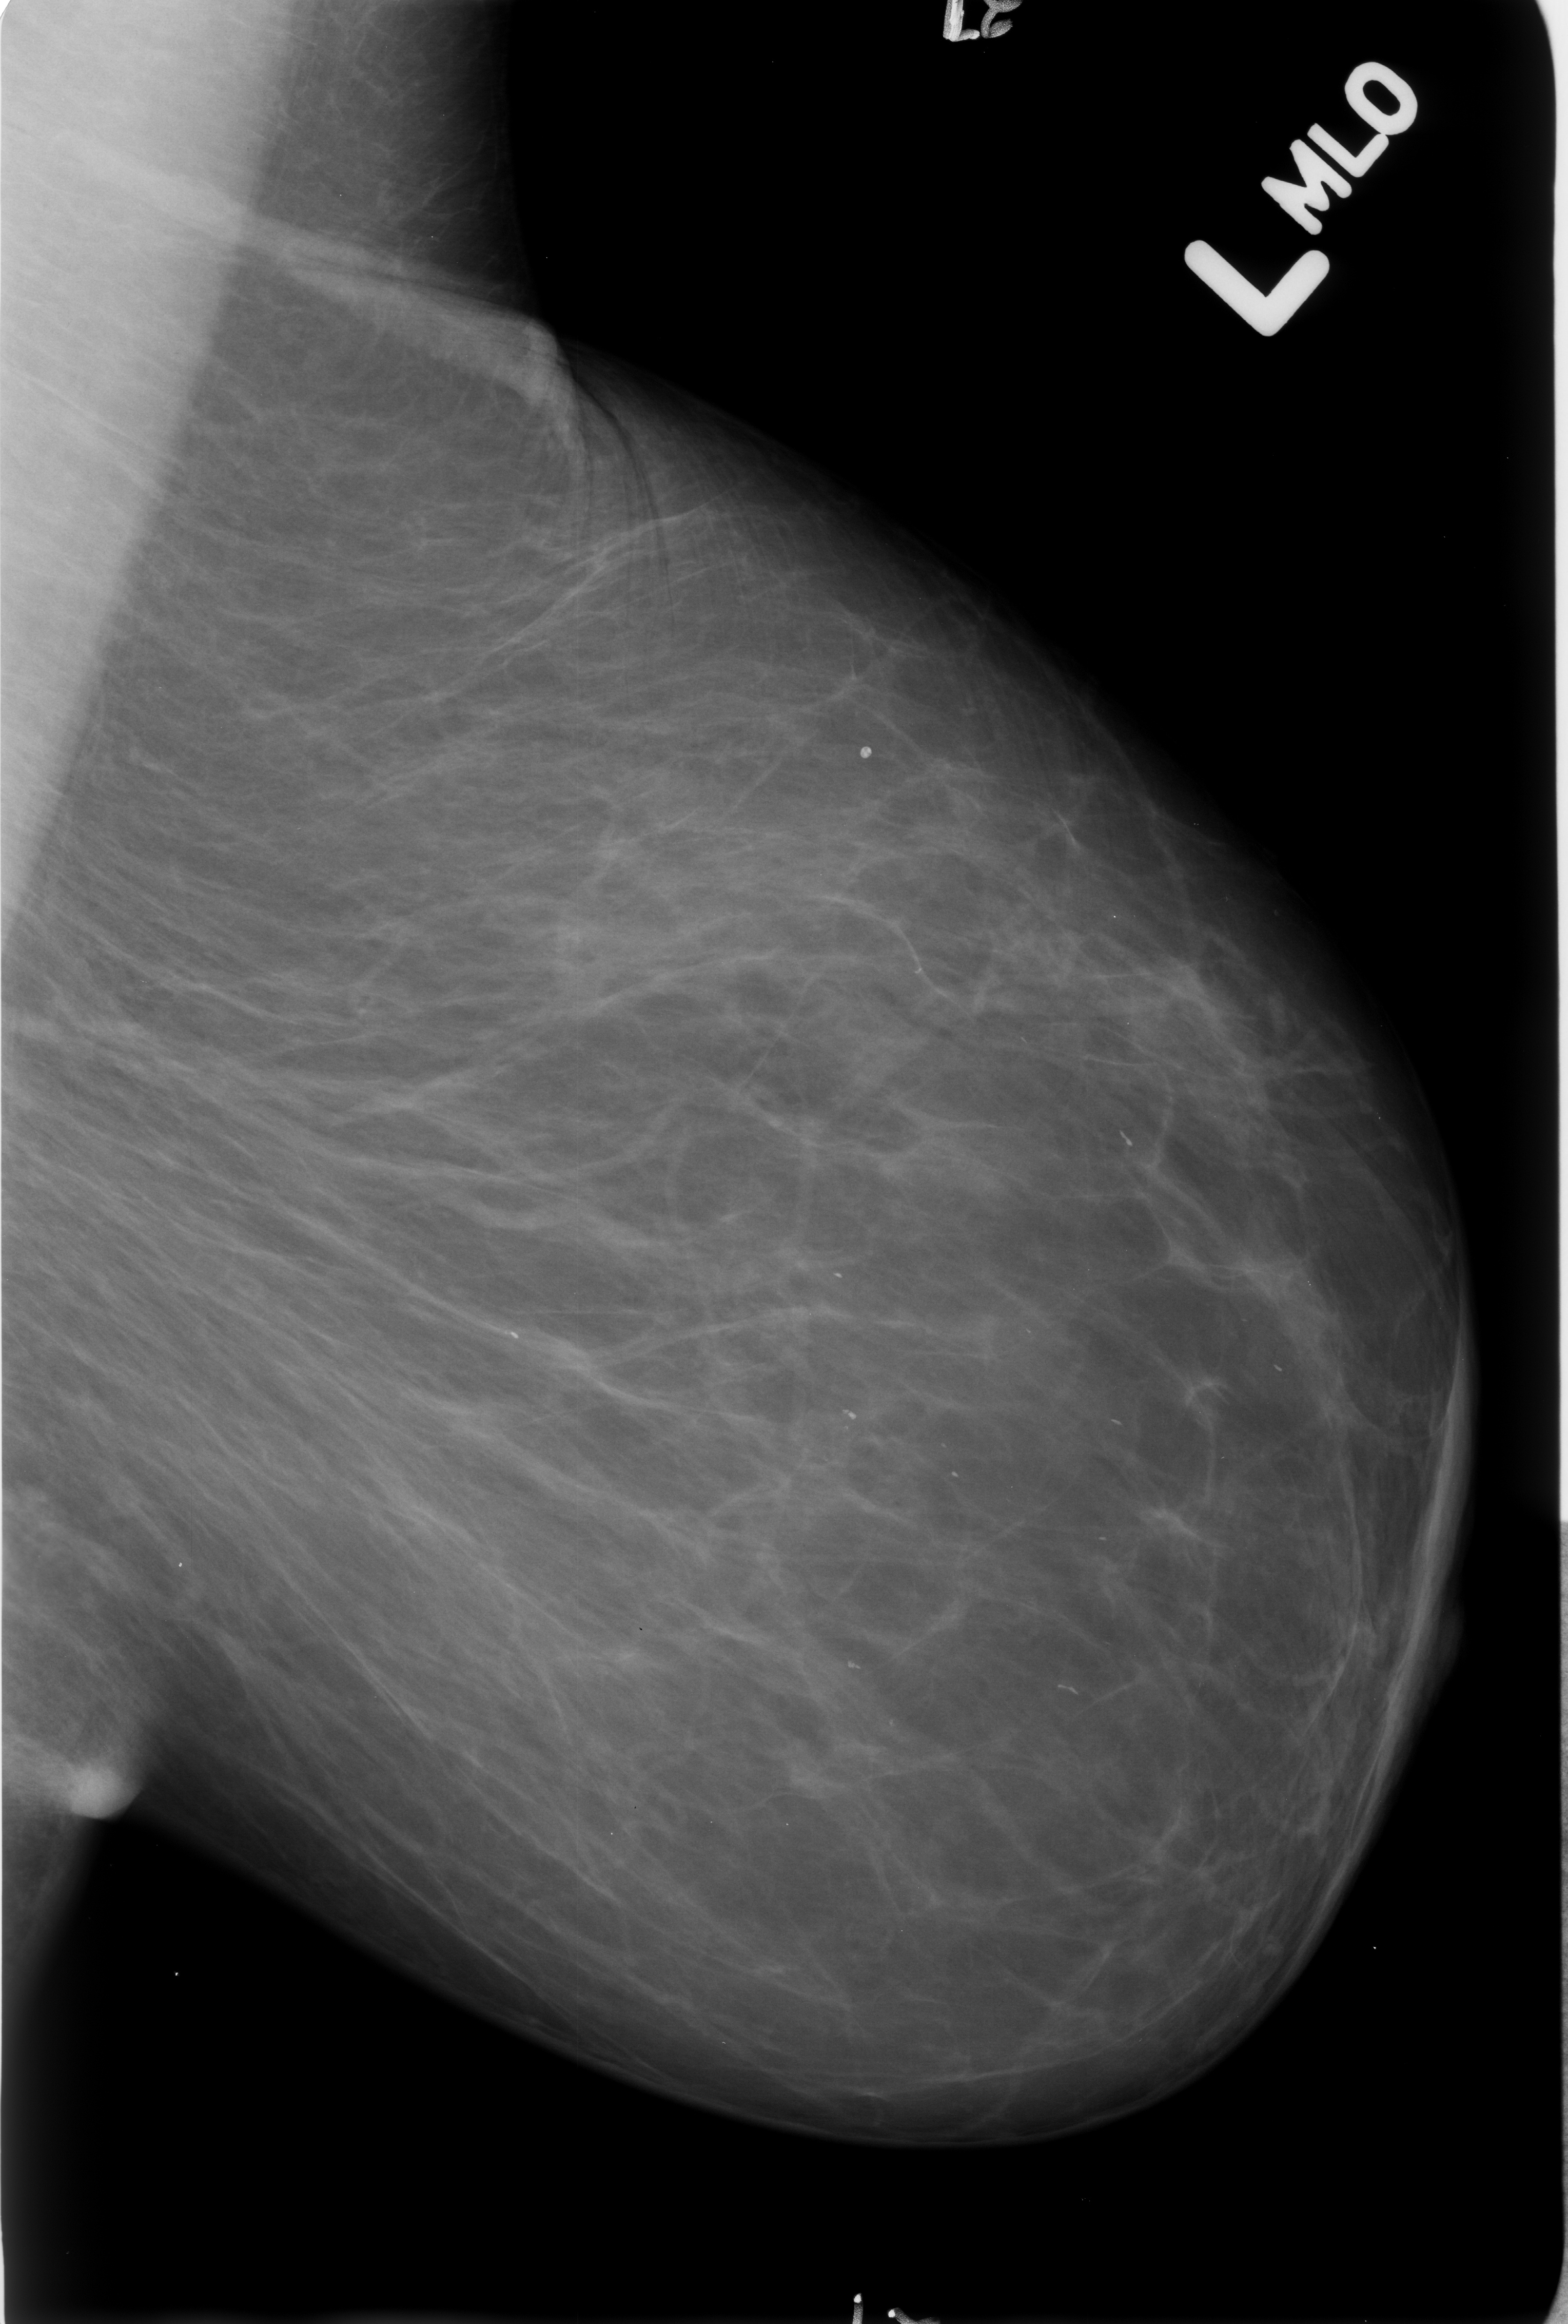
Digitized screen-film mammogram, left breast, MLO view.
Abnormality record for this image: Finding 1 of 3: calcifications, distribution regional; BI-RADS assessment category 2; benign without callback (not worked up further). Finding 2 of 3: calcifications, distribution regional; BI-RADS assessment category 2; benign; no additional work-up was recommended (benign without callback). Finding 3 of 3: calcifications, distribution regional; BI-RADS assessment category 2; subtlety rating 3 on a 1 (subtle) to 5 (obvious) scale; benign without callback (not worked up further).